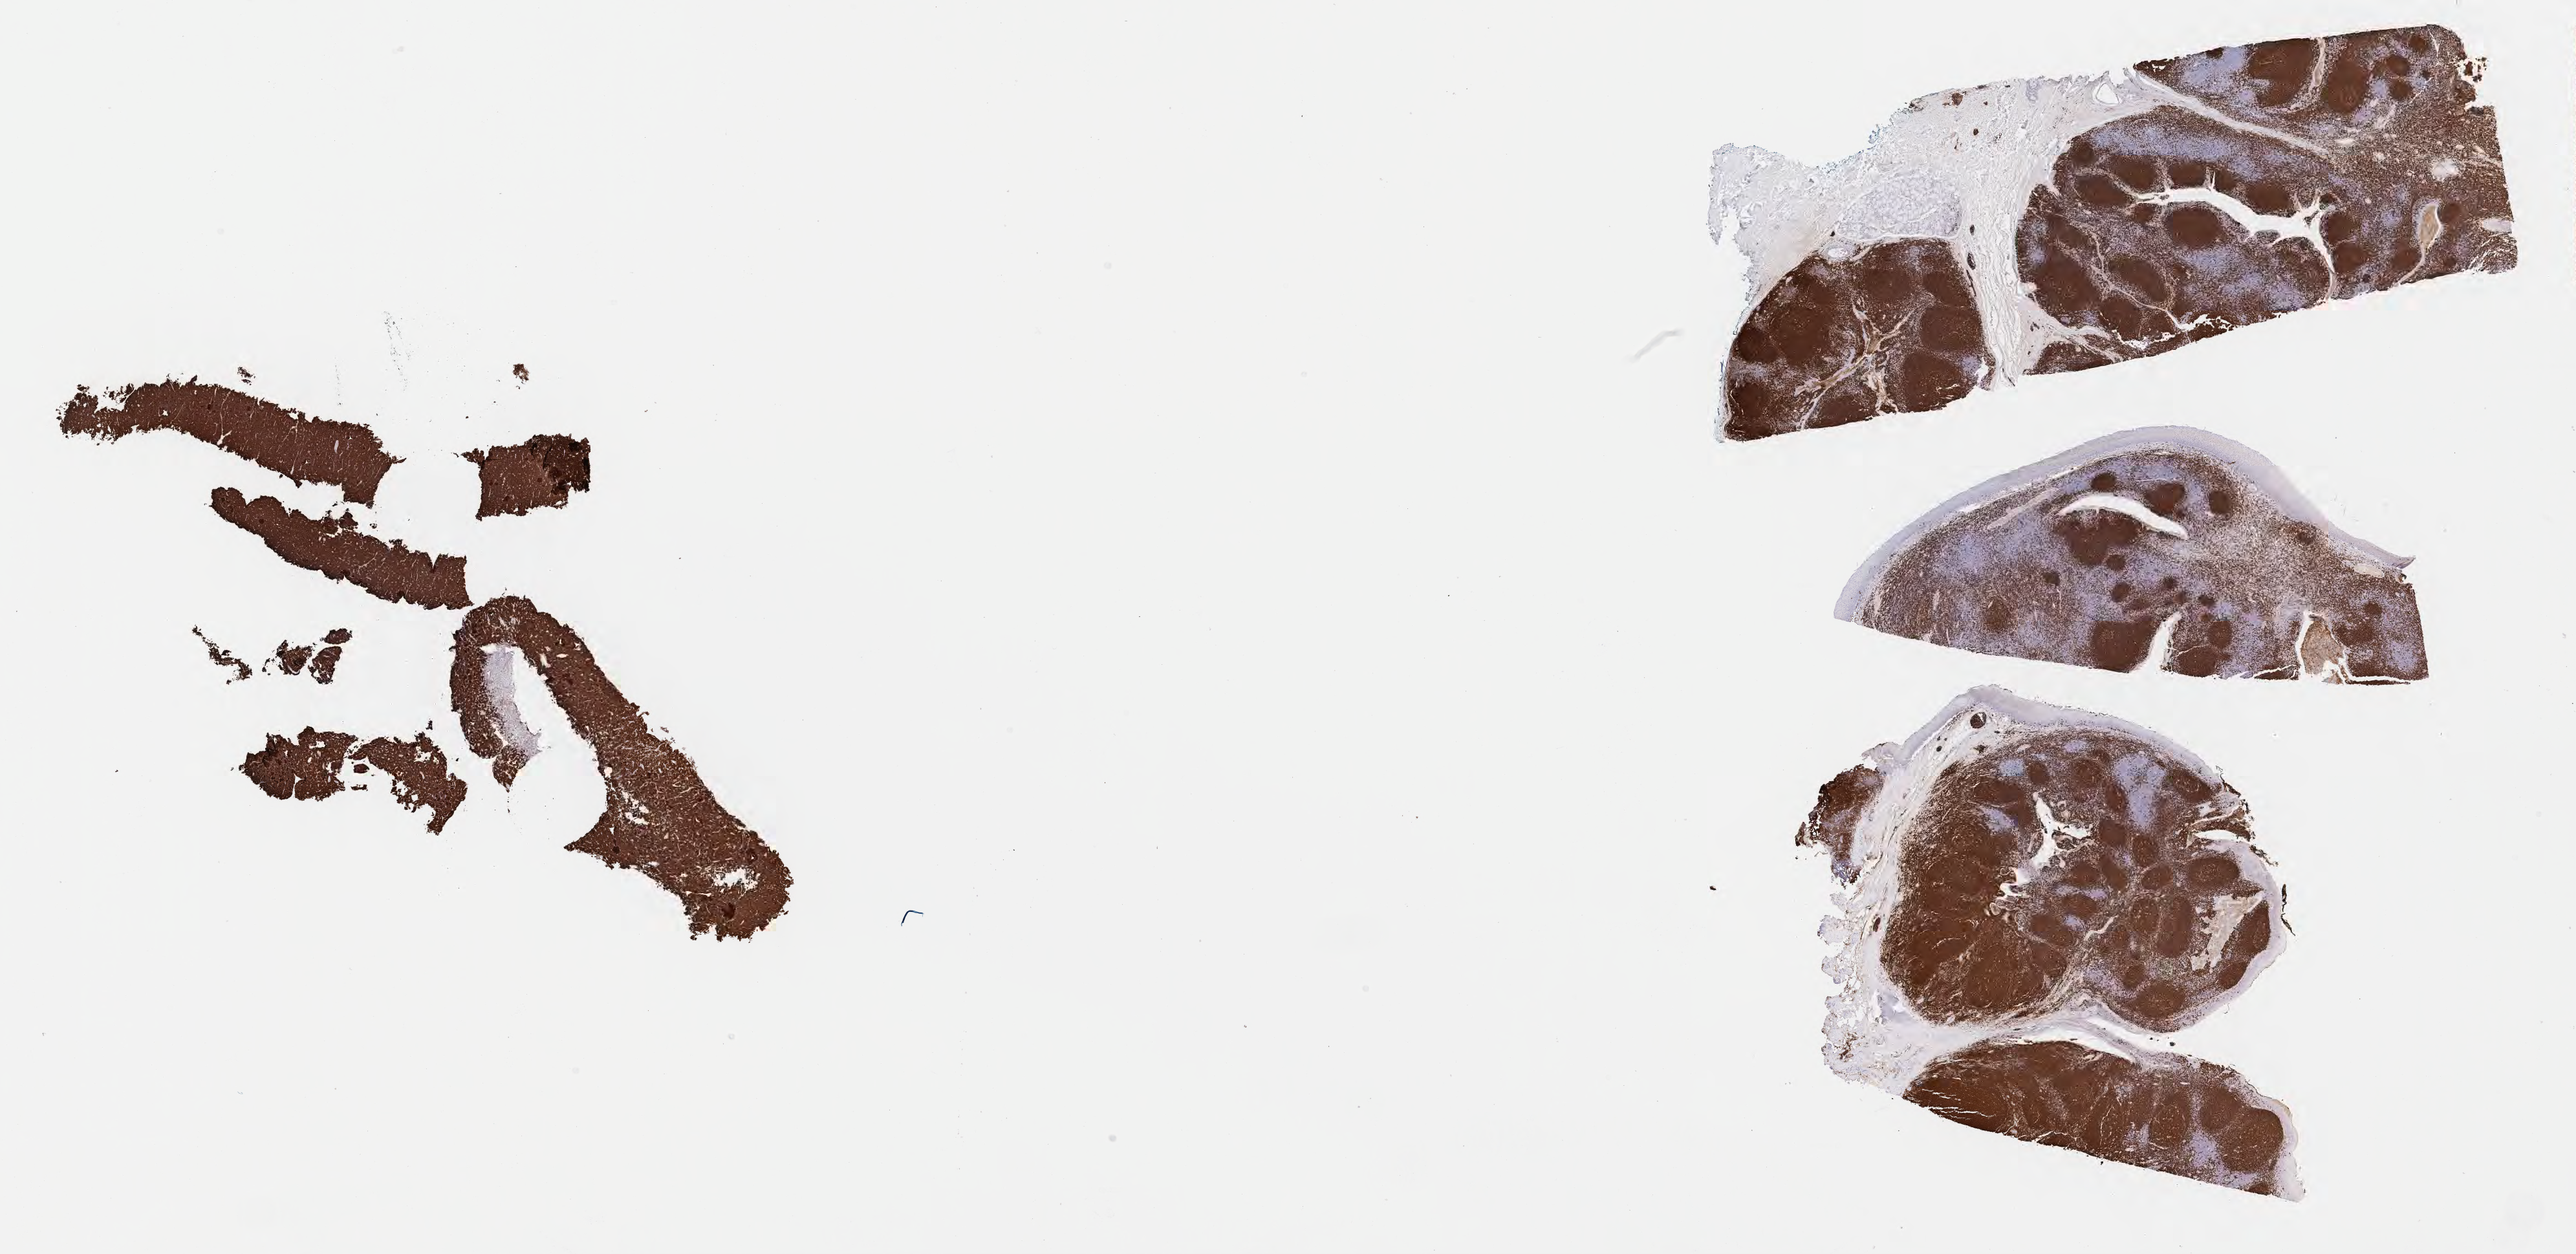
Immunohistochemistry (IHC) whole-slide image stained for CD20, whole scanned area (about 32.2 x 15.7 mm) shown as a low-resolution overview; specimen: tumor tissue; anatomic site: liver. Patient: male, age at initial diagnosis 4 years.
Histologic diagnosis: Burkitt lymphoma, NOS.